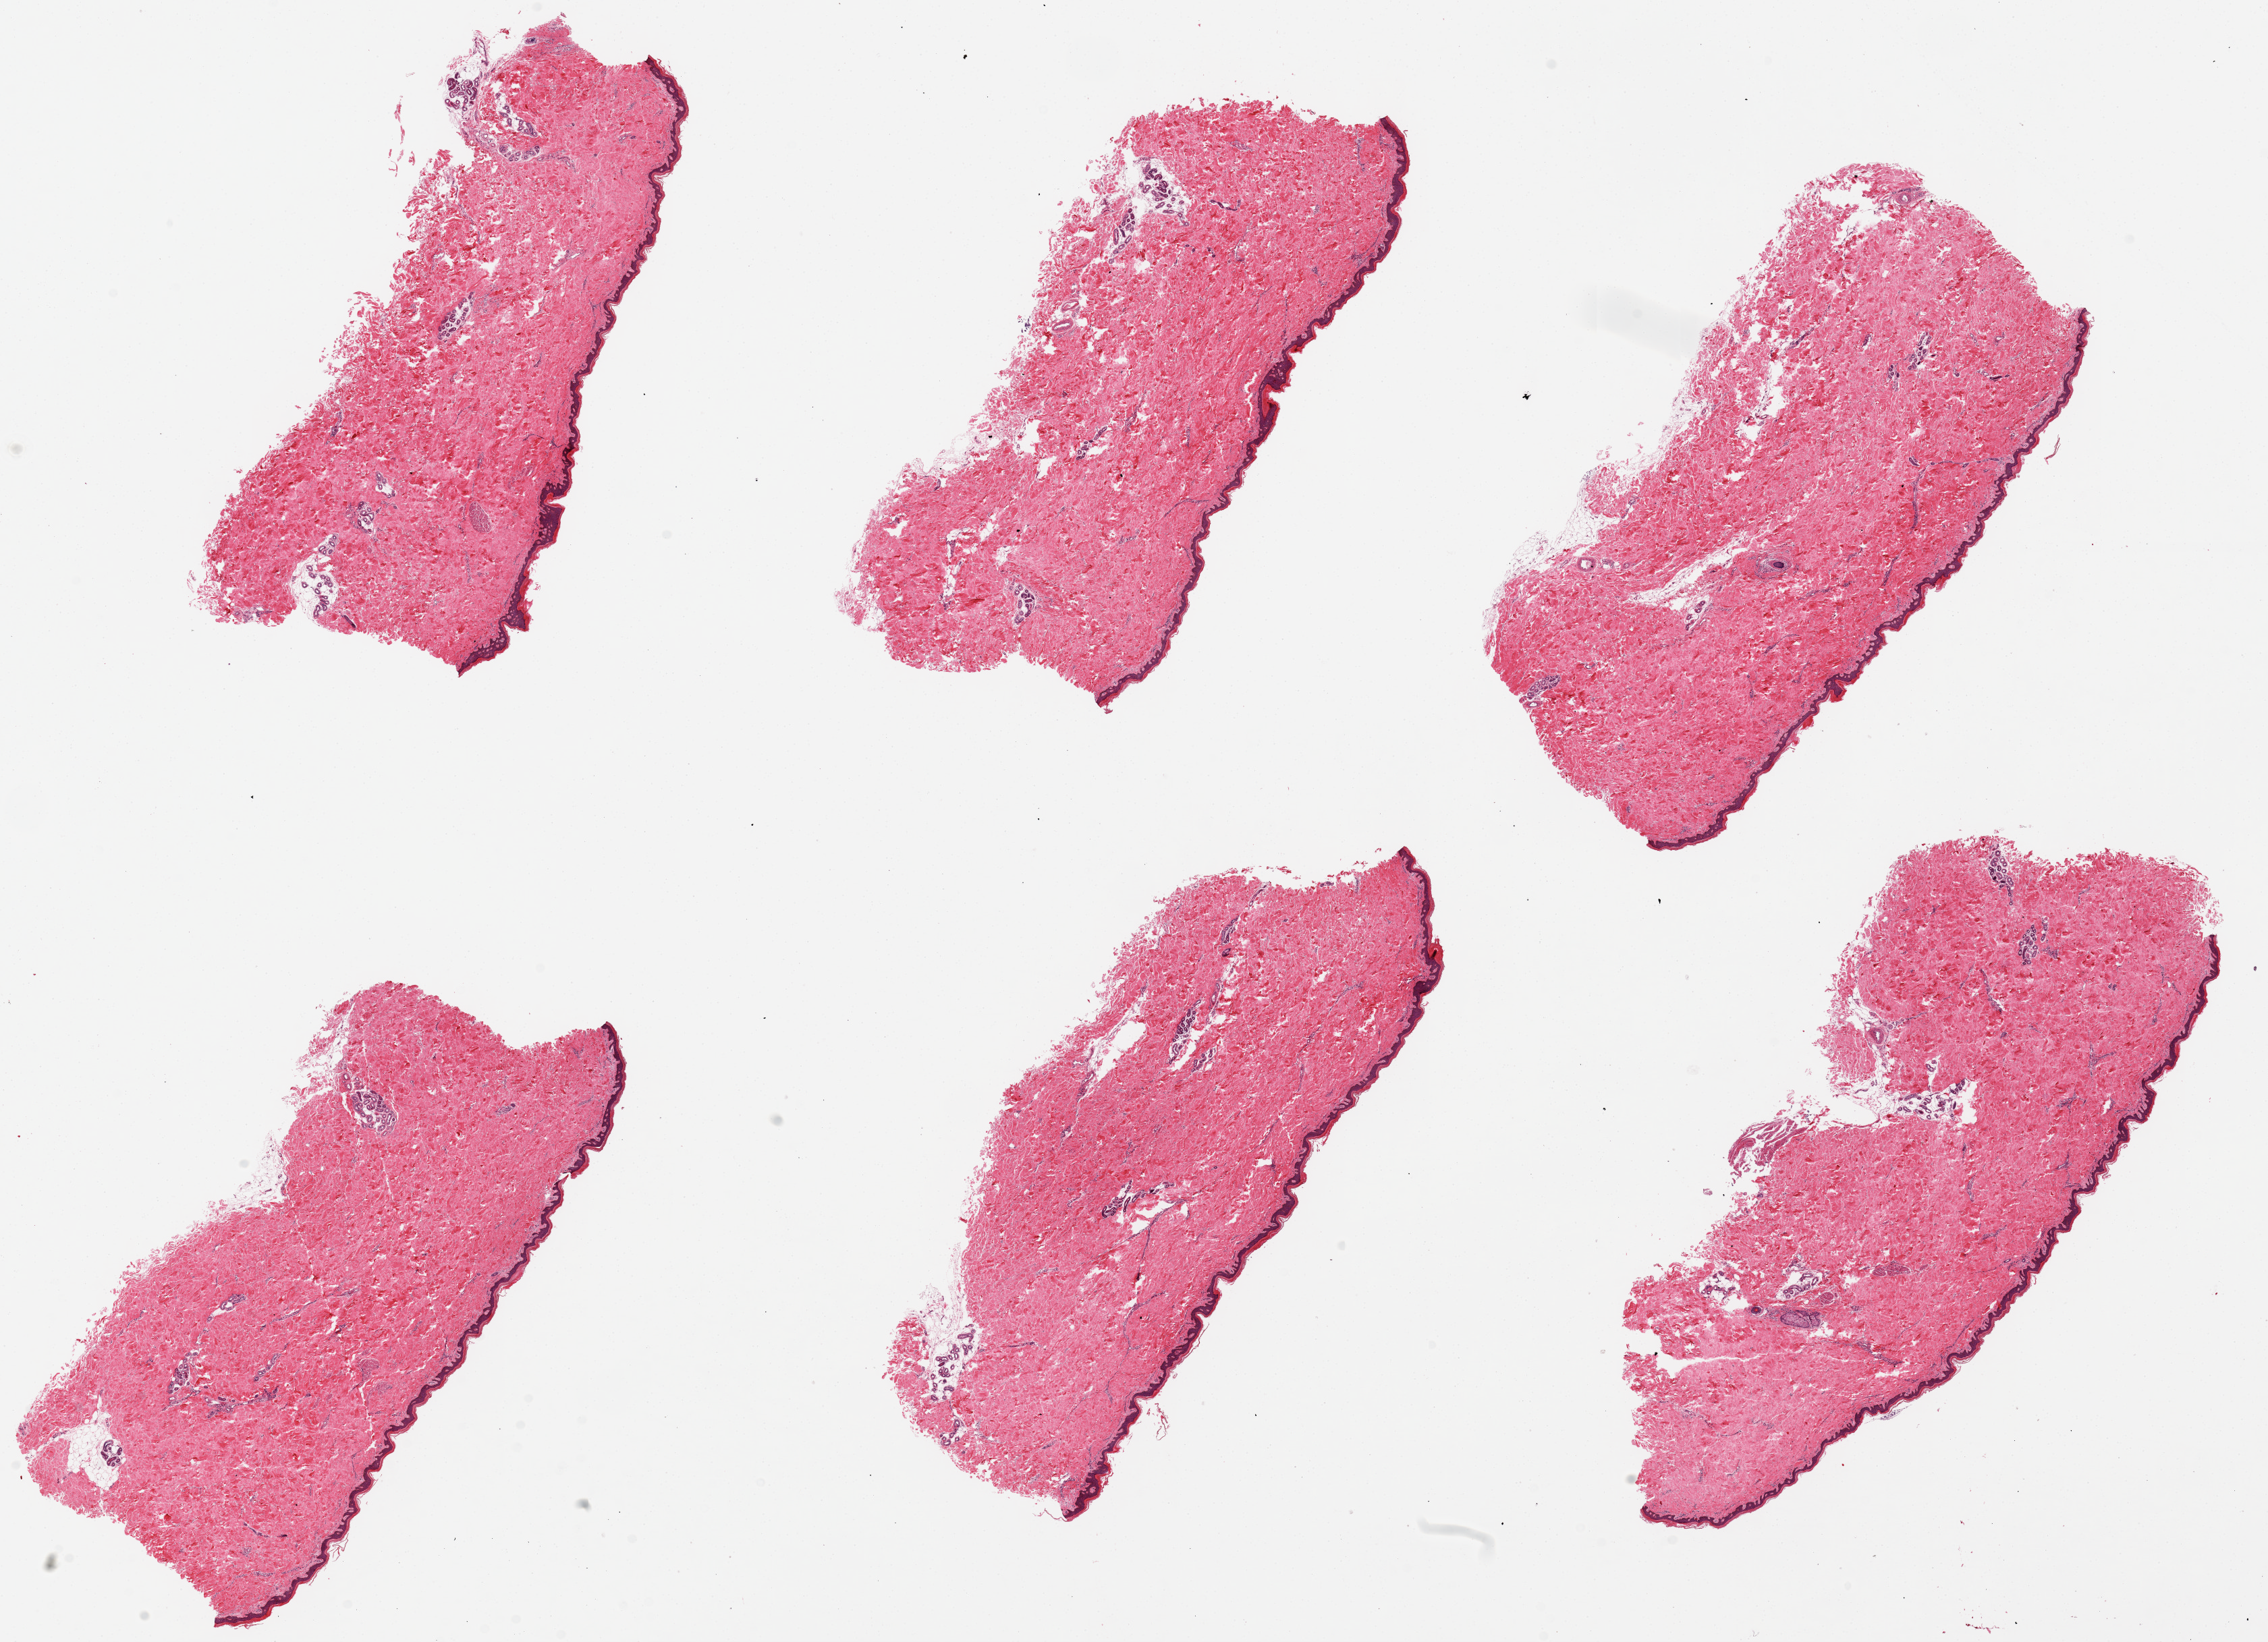
Digitized haematoxylin and eosin-stained section, shown as a low-resolution overview of the whole scanned area (about 26.6 x 19.2 mm); PAXgene-fixed, paraffin-embedded tissue; sampled site (target tissue): skin of suprapubic region; donor tissue sample. Donor sex: female.
• pathologist's review note for this sample: 6 pieces, up to 10x4mm. Well trimmed